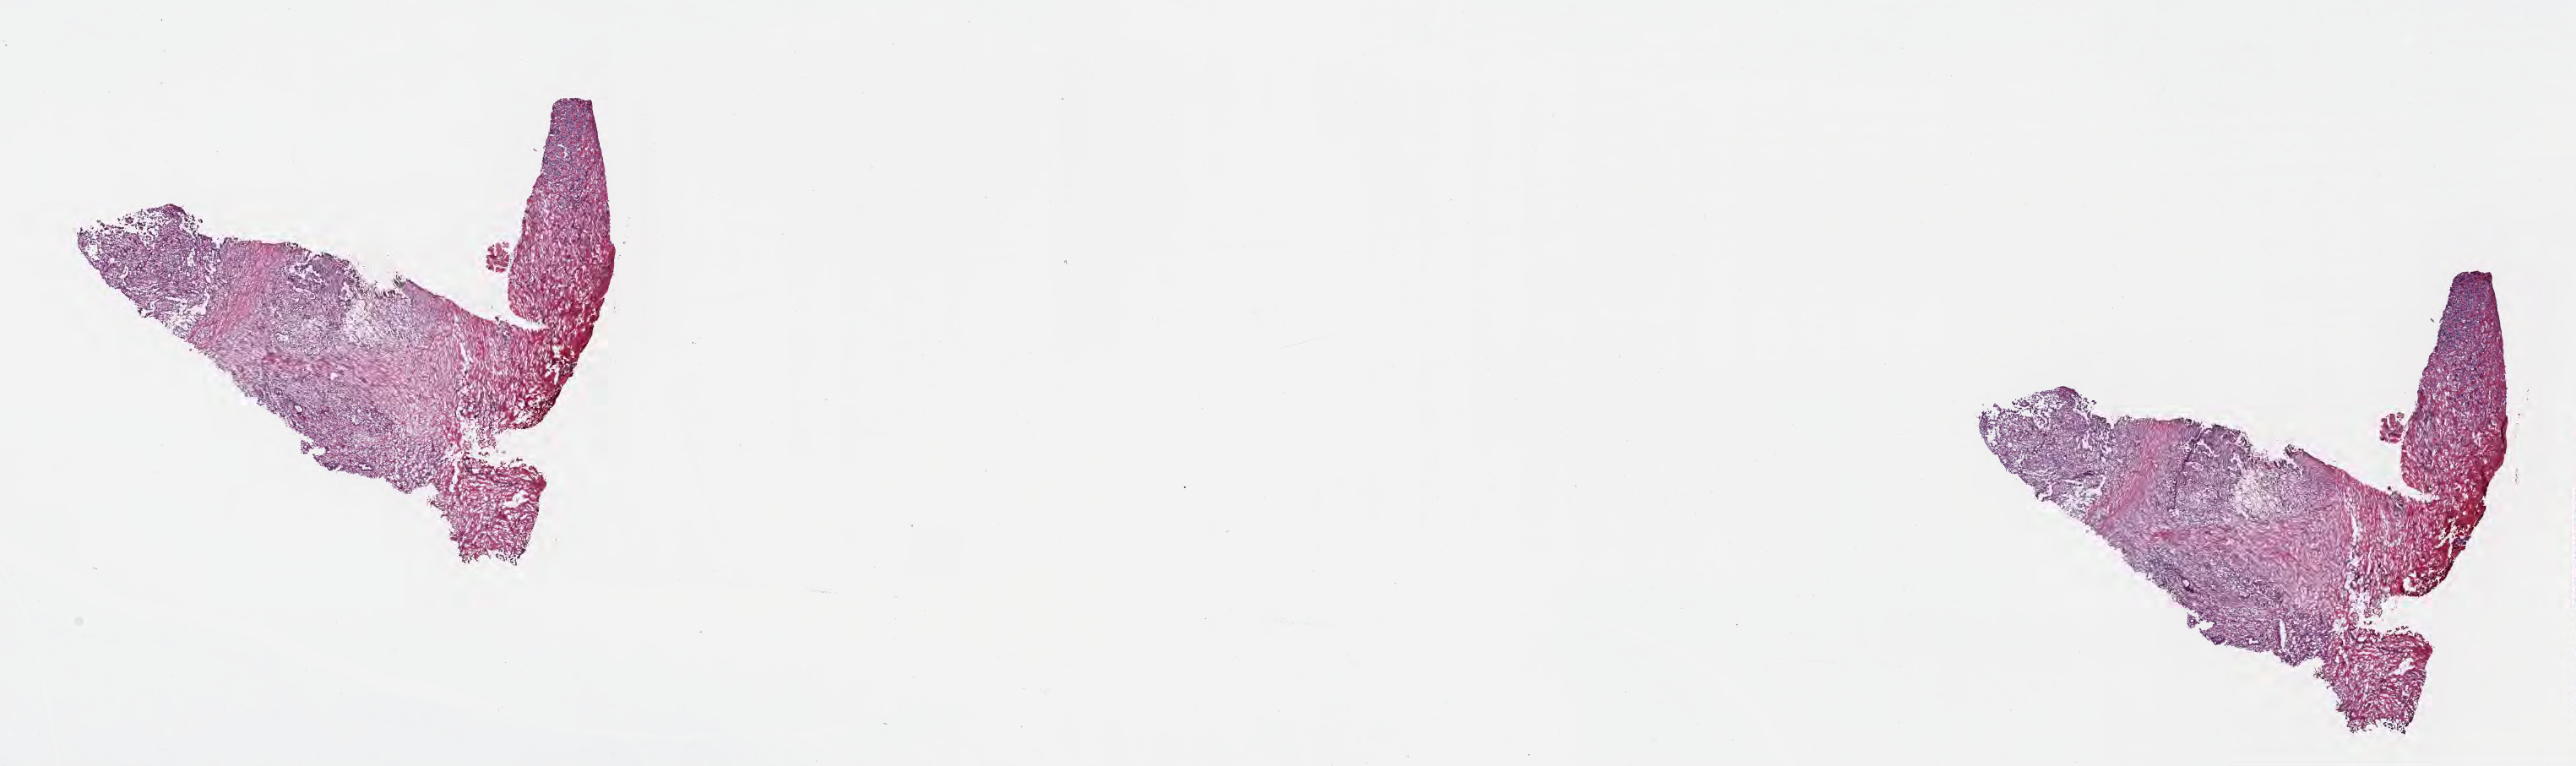
Haematoxylin and eosin whole-slide image, a low-resolution overview of the entire scanned area, about 24.6 x 7.3 mm, frozen section (tissue freezing medium), primary tumor, site: head of pancreas. Male, age 54 years at initial diagnosis. Tumor grade: G2 (moderately differentiated). Slide review estimates, as recorded: tumor cells 25%, tumor nuclei 30%, stromal cells 60%, necrosis 5%, normal cells 10%. Inflammatory infiltration, as recorded: lymphocyte infiltration 6%, monocyte infiltration 2%, neutrophil infiltration 2%.
AJCC pathologic stage: Stage III. Histologic diagnosis: Infiltrating duct carcinoma, NOS.